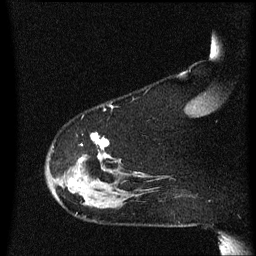
Breast MRI (dynamic contrast-enhanced), one sagittal slice. Slice 50 of 60 in the series (ordered by position). Dynamic contrast-enhanced series, image 2 of 3 at this slice position (ordered by acquisition). 1.5 T. TE 4.2 ms, TR 8.4 ms. 256 × 256 image matrix, field of view 200 × 200 mm. Patient: female, 48 years.
Structures marked on this image (semi-automatic segmentation, software-assisted and operator-edited):
- analysis volume of interest (the breast-tissue region the enhancement analysis was run in; not a lesion): box from (x=46, y=134) to (x=134, y=209) px
- tumour enhancement mask (voxels above the 70 % enhancement threshold inside the analysis volume of interest): (x=69, y=134)–(x=109, y=185)